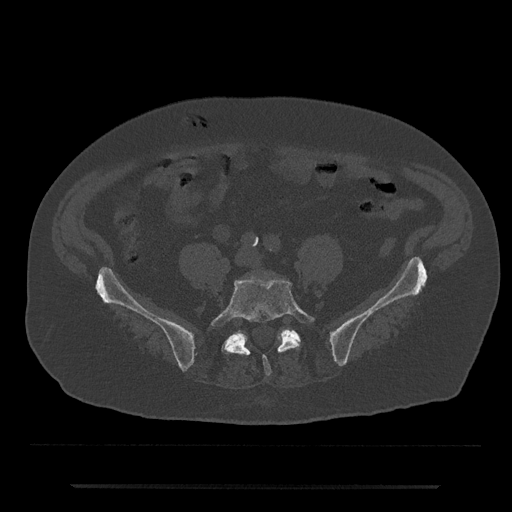
CT including the spine, one axial slice; position 282 of 797 along the scan axis; reconstruction kernel Br40s/3; 120 kVp; bone window (W 1800 / L 400 HU); 0.5 mm slice thickness; 512 × 512 image matrix, field of view 434 × 434 mm. Male patient, age 80 years. From the clinical record (not read from this slice): primary cancer: prostate; vertebrae with lytic lesions (as recorded): L1, T11.
Structures marked on this image (semi-automatically segmented with operator editing):
- L5 vertebra: bounding box (x1, y1, x2, y2) in pixels: (210, 277, 315, 376)